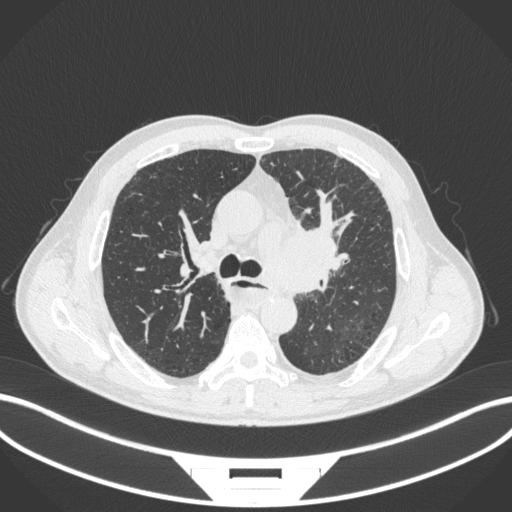
Chest CT, one axial slice. Position 249 of 411 along the scan axis. Reconstruction kernel B31f. Lung window (W 1500 / L -600 HU). 1 mm slice thickness. 512 × 512 image matrix, field of view 400 × 400 mm. Patient: male, 57 years. Case-level facts recorded for this patient, not image findings: clinical TNM (as recorded): T2a N1 M0.
Annotated regions visible in this slice (rectangle marked by the reading radiologist):
- lung tumour (recorded histology: squamous cell carcinoma): bounding box [x1, y1, x2, y2] px = [259, 212, 351, 296]